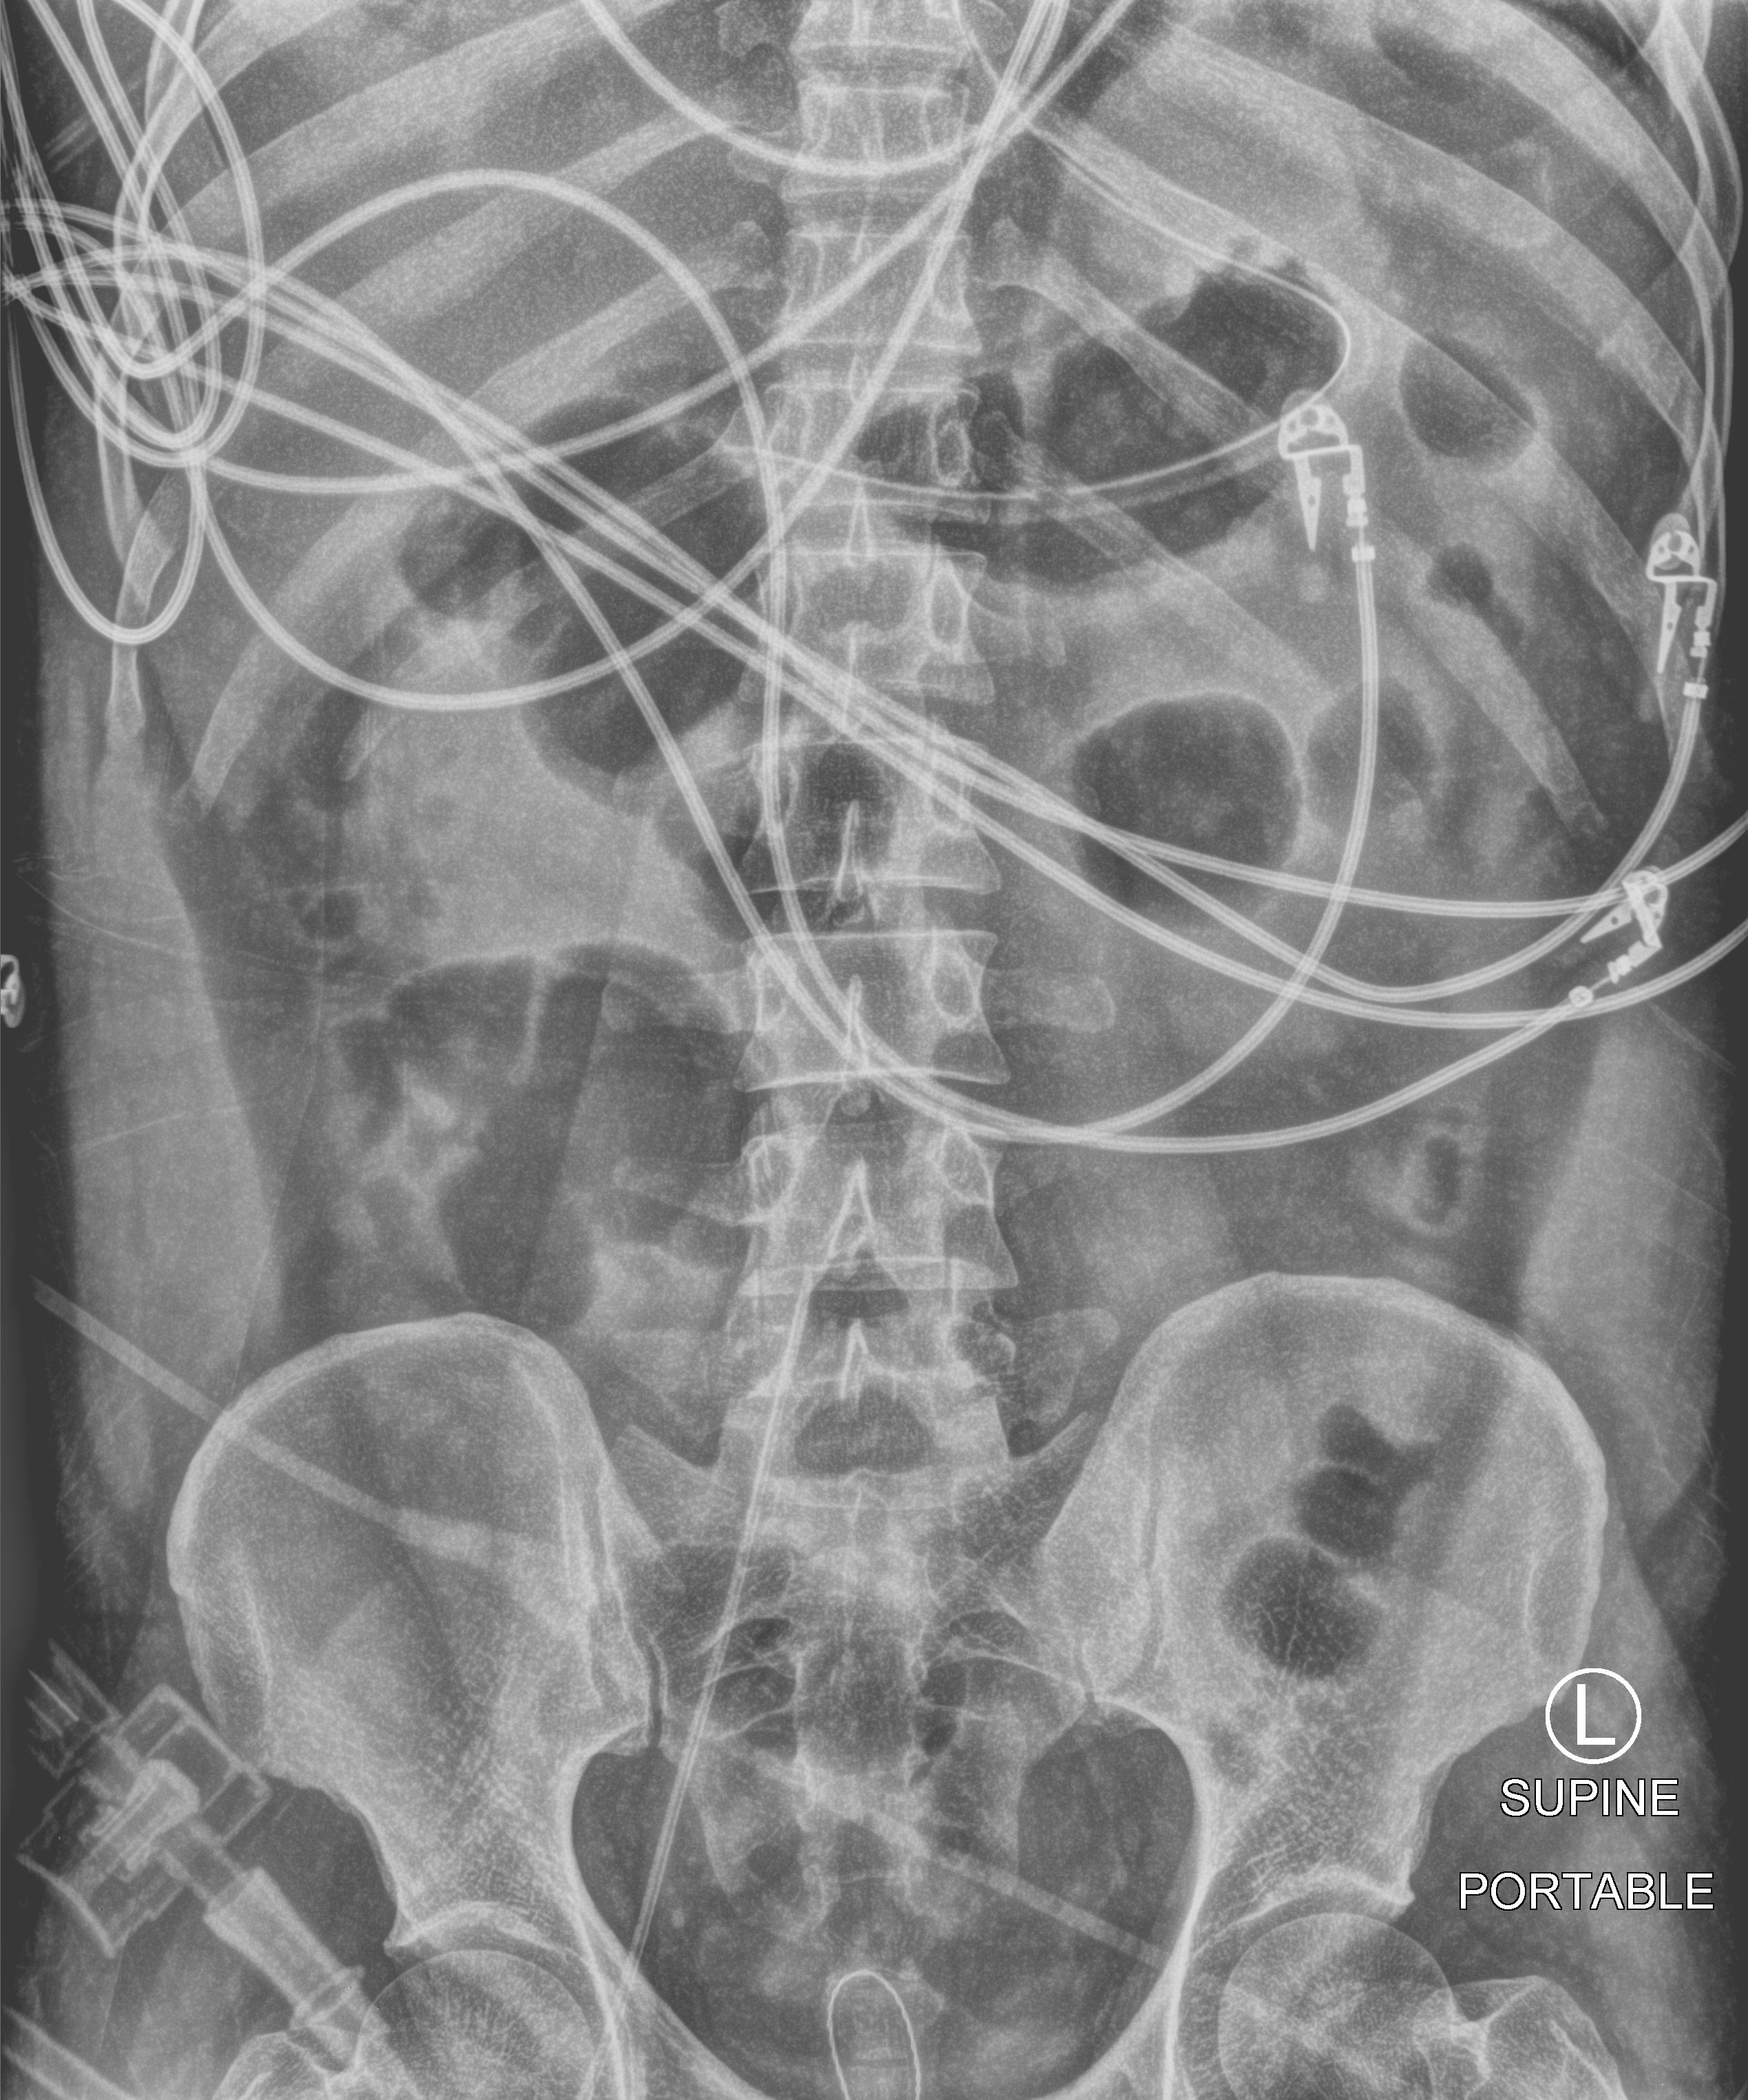
Bedside abdomen radiograph (computed radiography); anteroposterior (AP) projection. Patient hospitalised with COVID-19; male, aged 18–59 years.
Hospital-stay facts (about this admission, not read from this image; timing relative to this image not recorded): mechanically ventilated during this hospital stay: yes.